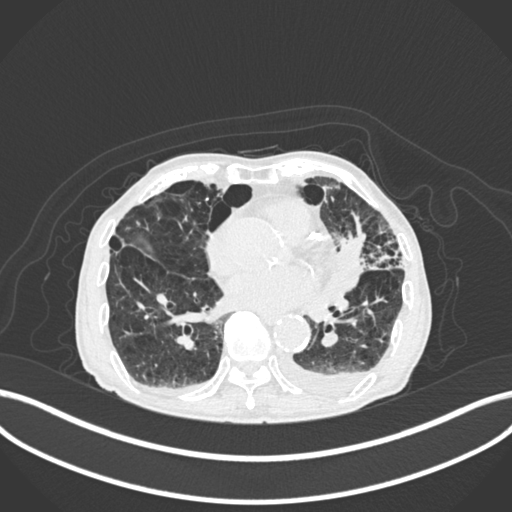
Chest CT, one axial slice; 120 kVp; lung window (W 1500 / L -600 HU); 1 mm slice thickness; 512 × 512 image matrix, field of view 400 × 400 mm. Male patient, age 90 years or older. From the clinical record (not read from this slice): clinical TNM (as recorded): T2b N1 M0.
Structures marked on this image (rectangle marked by the reading radiologist):
- lung tumour (recorded histology: squamous cell carcinoma): bounding box (x1, y1, x2, y2) in pixels: (335, 225, 368, 292)